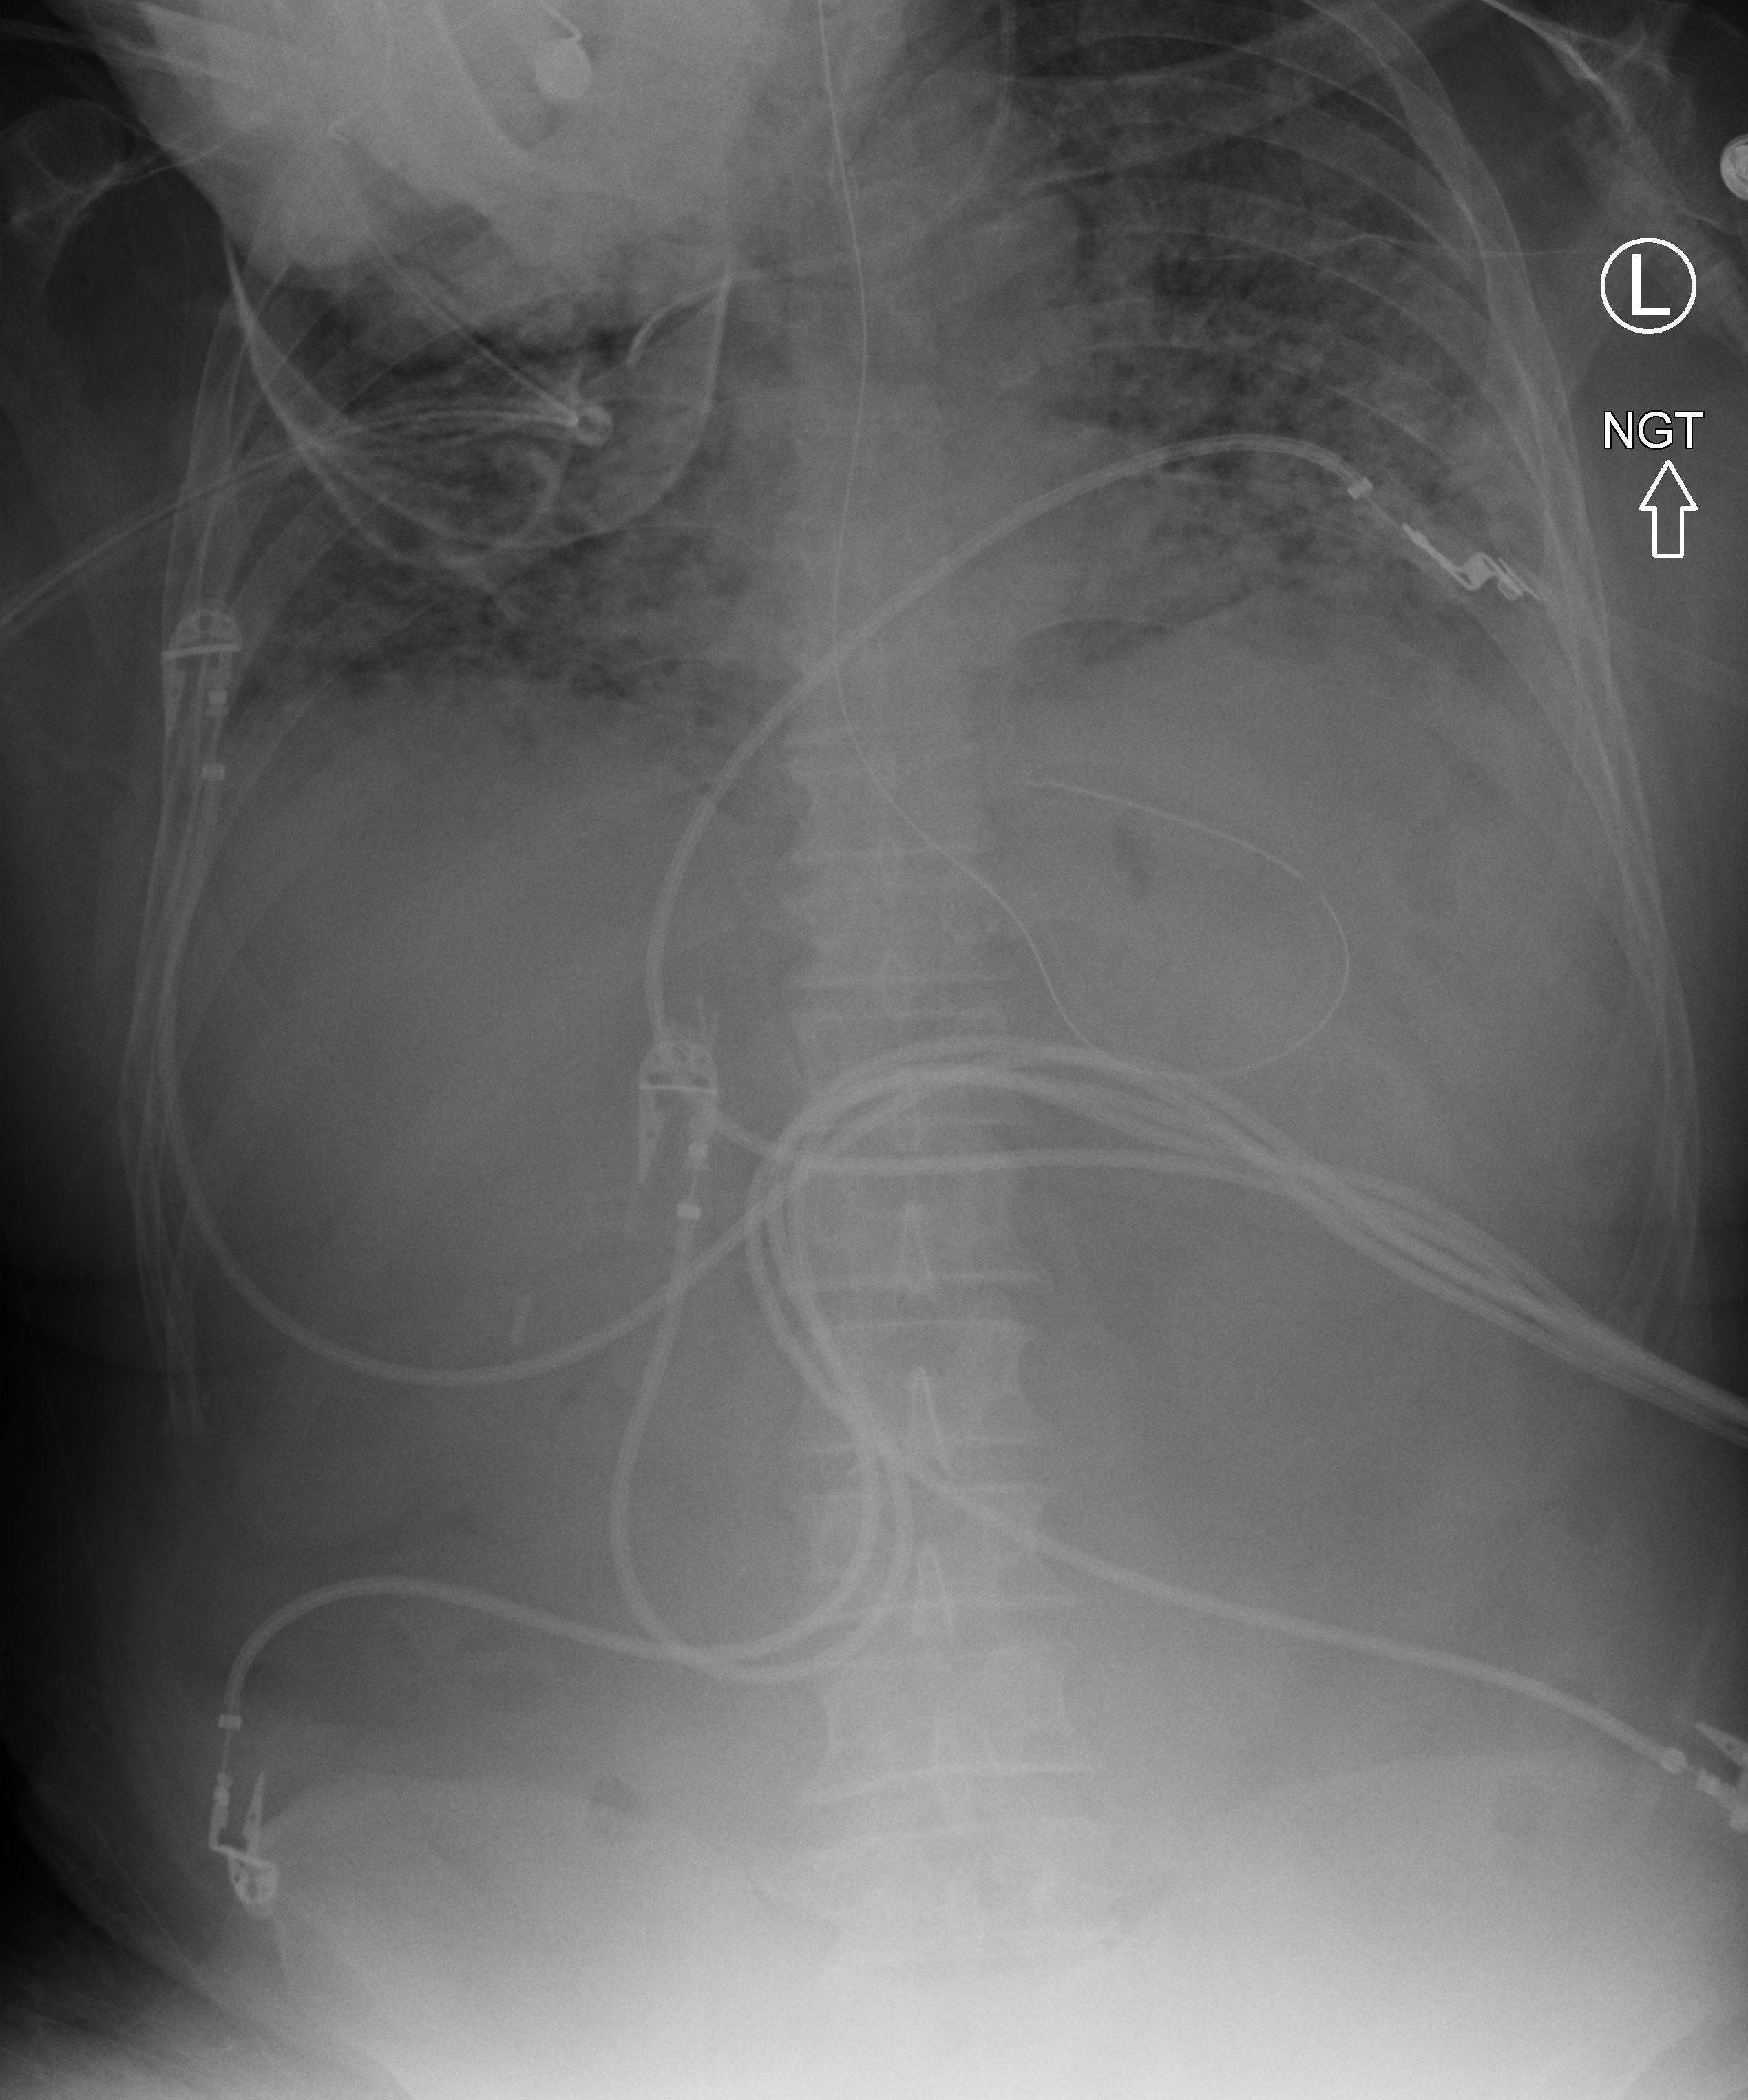
Portable chest radiograph, anteroposterior (AP) projection. Male patient hospitalised with COVID-19, age 60–74 years.
Hospital-stay facts (about this admission, not read from this image; timing relative to this image not recorded):
- length of hospital stay: 23 days